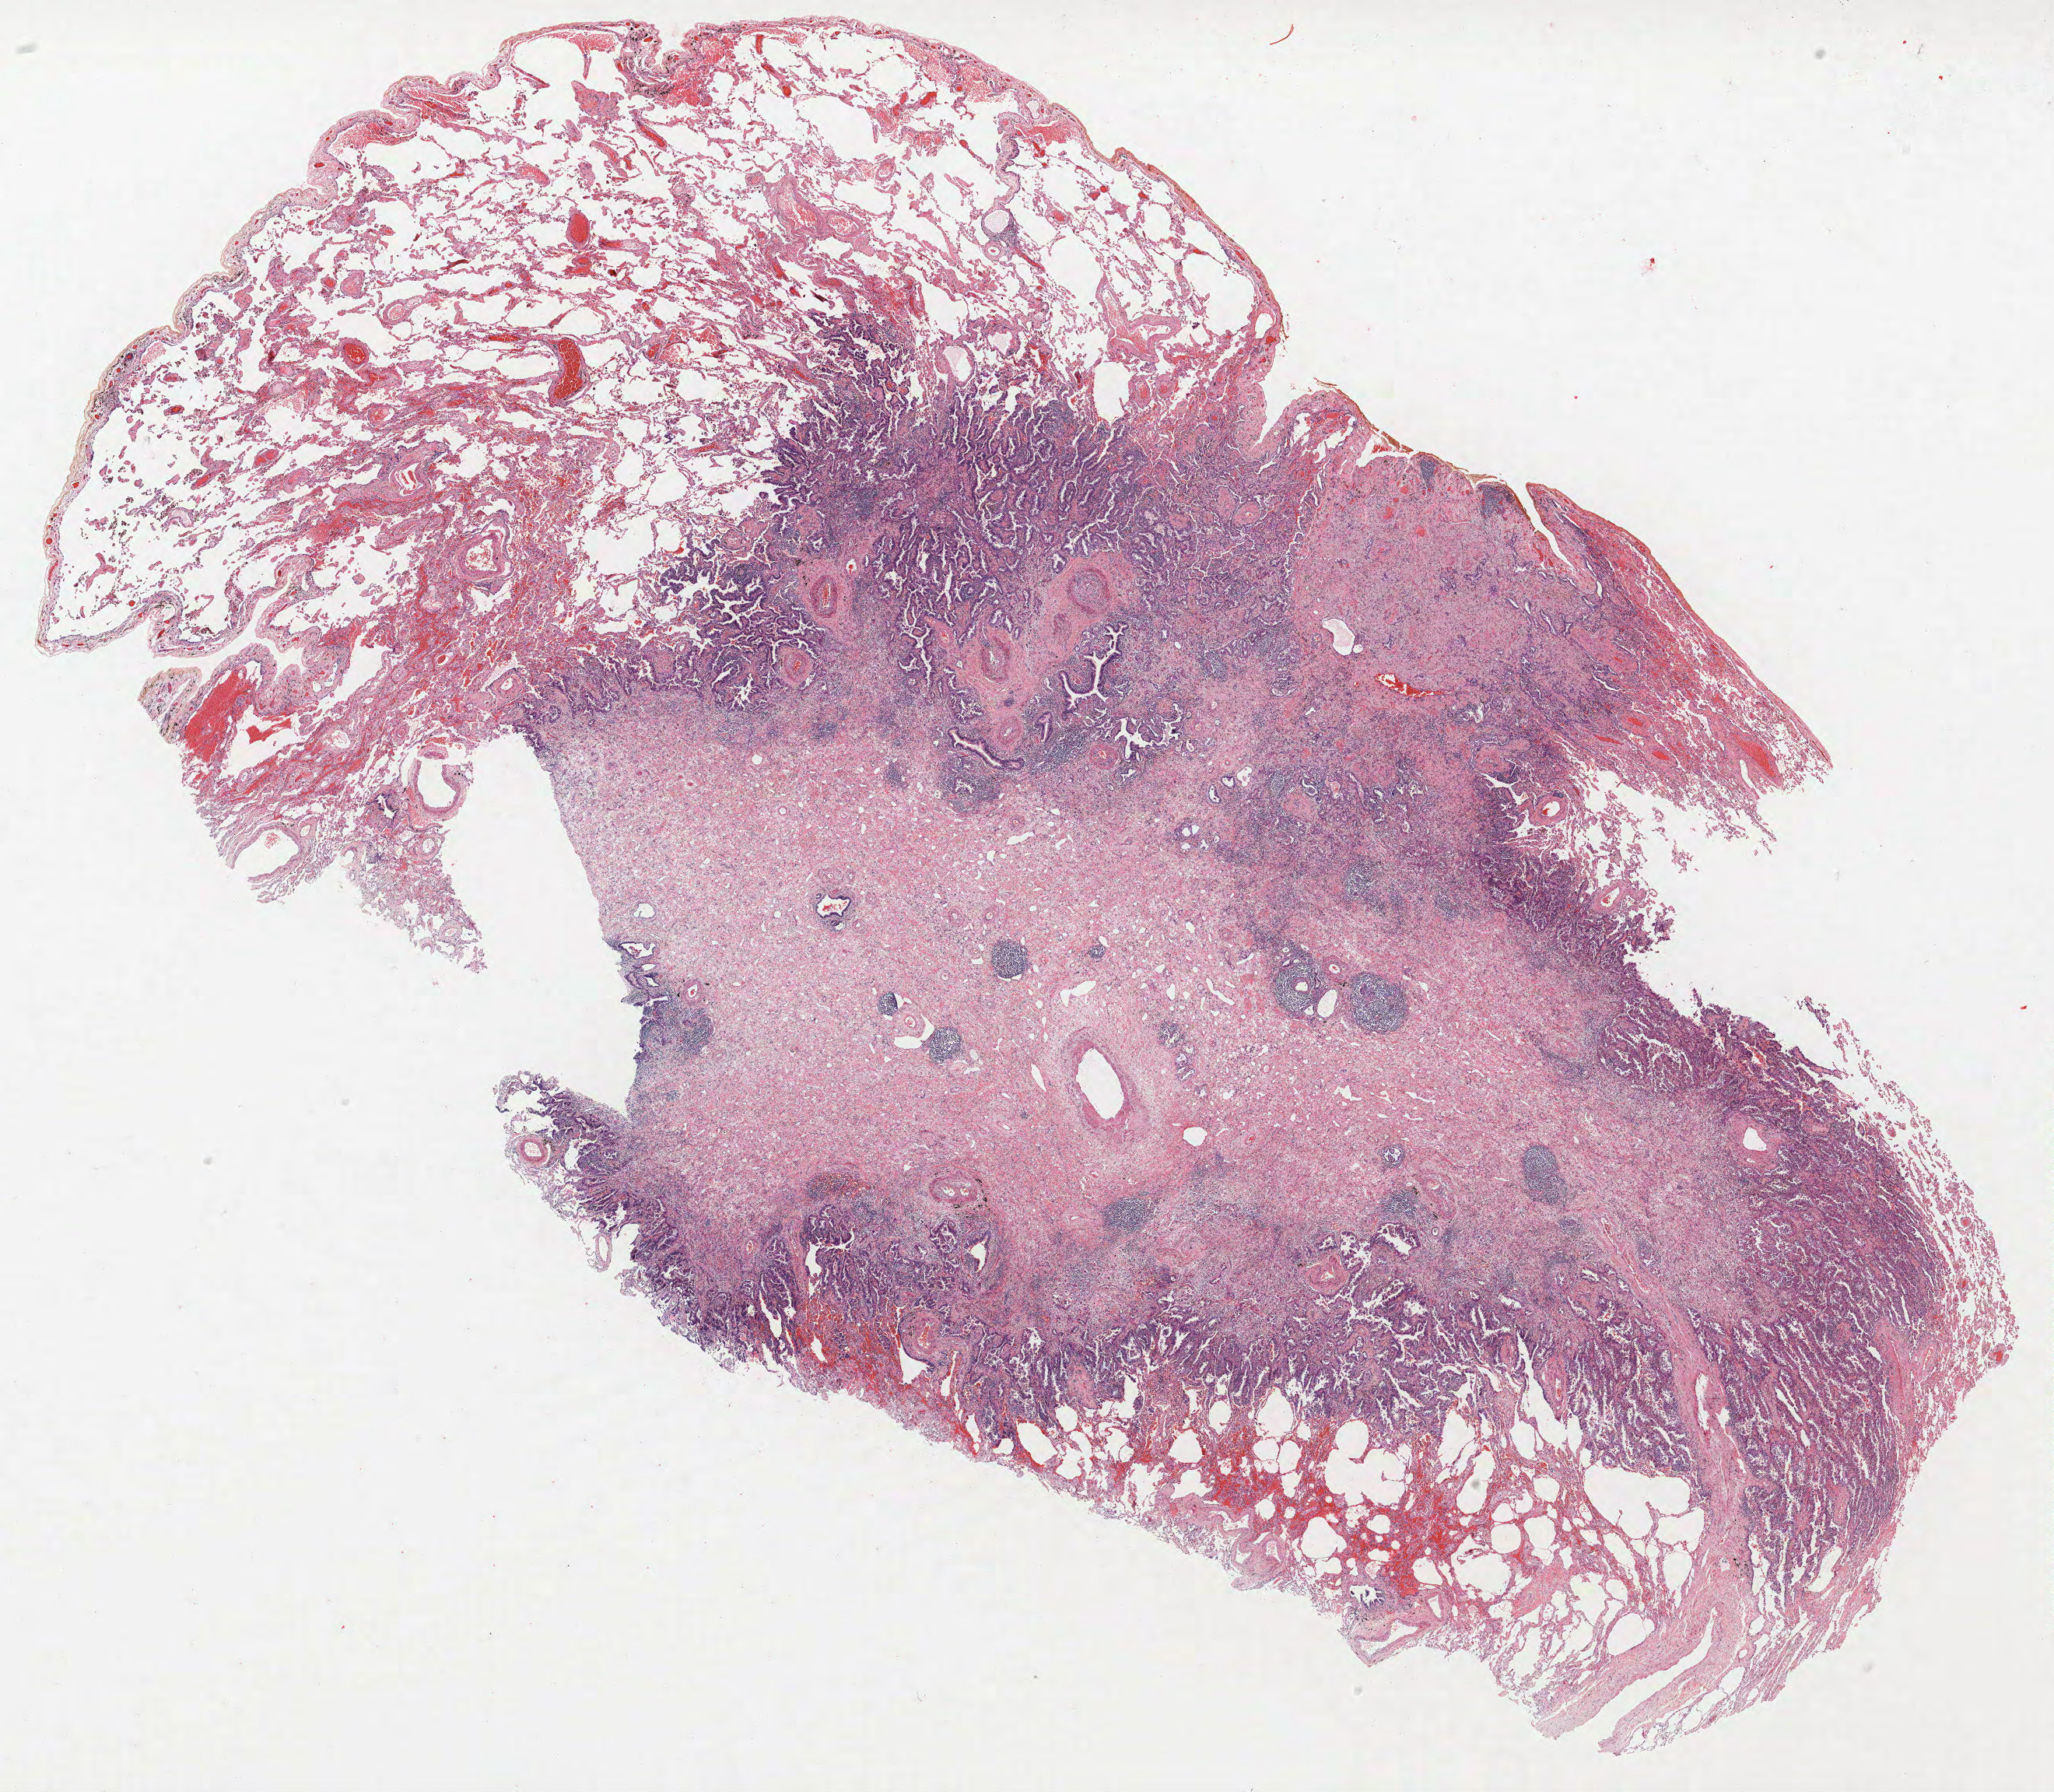
Whole-slide histology image, H&E, low-resolution overview of the scanned area, about 21.1 x 18.4 mm (slide scanned at 40x). FFPE section. Lung. Male, age 74 at enrolment. Grade: moderately differentiated (G2).
Primary tumour location (clinical record): right lower lobe. Participant's lung-cancer diagnosis: Bronchiolo-alveolar adenocarcinoma, NOS. Tumour size (pathology): 16 mm. Stage (AJCC 6th edition): IA.